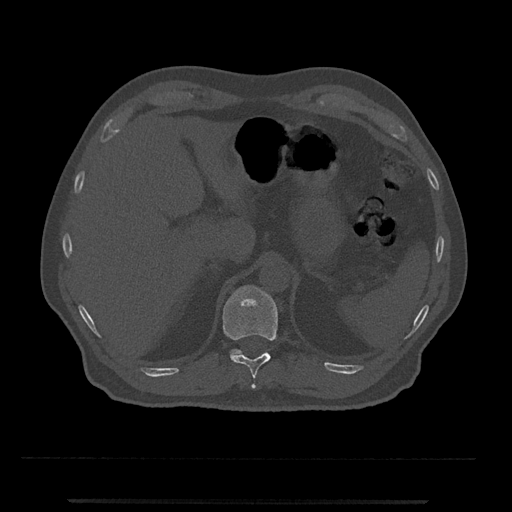
CT including the spine, one axial slice. Slice 453 of 797 in the series (ordered by position). Reconstruction kernel Br40s/3. Bone window (W 1800 / L 400 HU). 512 × 512 image matrix, field of view 419 × 419 mm. Male patient, age 63 years. From the clinical record (not read from this slice): primary cancer: prostate.
Structures marked on this image (semi-automatically segmented with operator editing):
- T11 vertebra: bounding box [x1, y1, x2, y2] px = [222, 285, 278, 389]
- T12 vertebra: [230, 349, 243, 355]